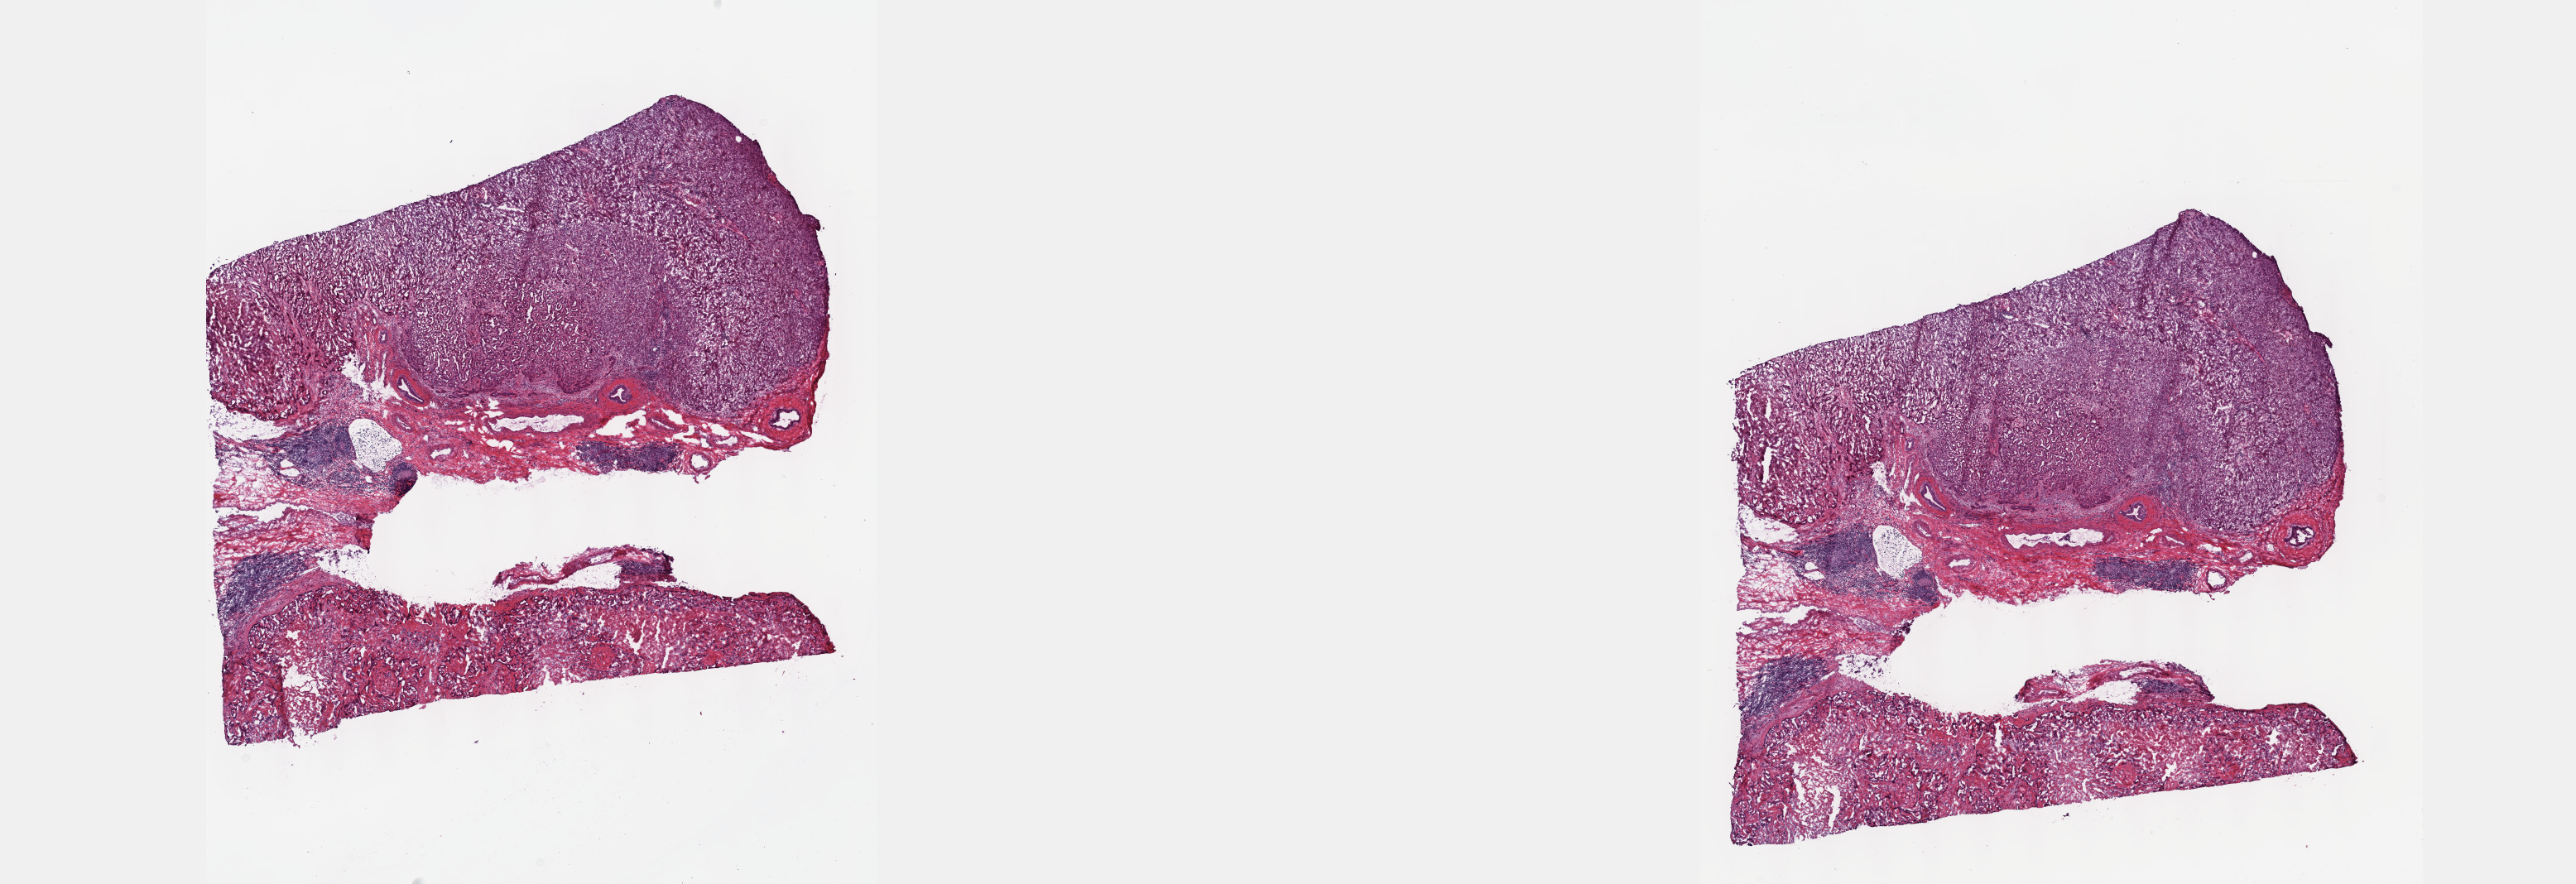
Whole-slide histology image, Hematoxylin and eosin (H&E) stained — low-resolution overview of the scanned area, about 25.1 x 8.6 mm (acquisition: 40x scan). Frozen section from the top of the tissue portion. Primary tumour sample from the bile duct. Male, age 73 years at initial diagnosis. Histologic grade: G2 (moderately differentiated). Composition of this section per pathologist review: tumour cells 85%, tumour nuclei 75%, normal cells 15%, stromal cells 0%, necrosis 0%. Infiltration values recorded for this section: lymphocyte infiltration 0%, monocyte infiltration 0%, neutrophil infiltration 0%.
• diagnosis: Cholangiocarcinoma
• AJCC pathologic stage: I (7th edition)